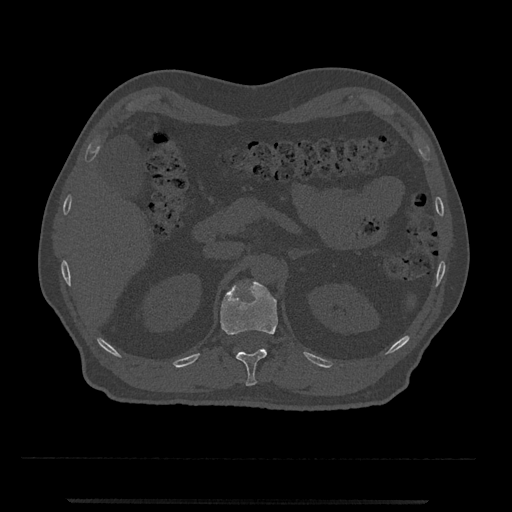
CT including the spine, one axial slice; position 386 of 797 along the scan axis; reconstruction kernel Br40s/3; 120 kVp; bone window (W 1800 / L 400 HU); 512 × 512 image matrix, field of view 419 × 419 mm. Male patient, age 63 years. From the clinical record (not read from this slice): primary cancer: prostate.
Outlined on this slice (semi-automatic segmentation, software-assisted and operator-edited):
- T12 vertebra: box from (x=220, y=280) to (x=278, y=386) px